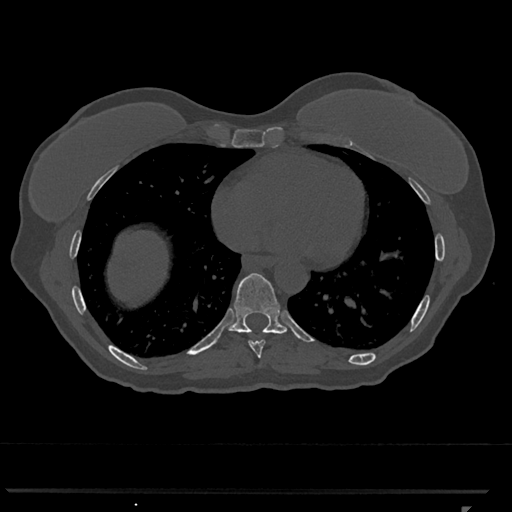
CT including the spine, one axial slice. Position 636 of 793 along the scan axis. 120 kVp. Bone window (W 1800 / L 400 HU). 0.5 mm slice thickness. 512 × 512 image matrix, field of view 380 × 380 mm. Female patient, age 62 years. From the clinical record (not read from this slice): primary cancer: renal.
Annotated regions visible in this slice (semi-automatic segmentation, software-assisted and operator-edited):
- T8 vertebra: bounding box <248,340,265,358> (left, top, right, bottom; pixels)
- T9 vertebra: <228,273,297,337>